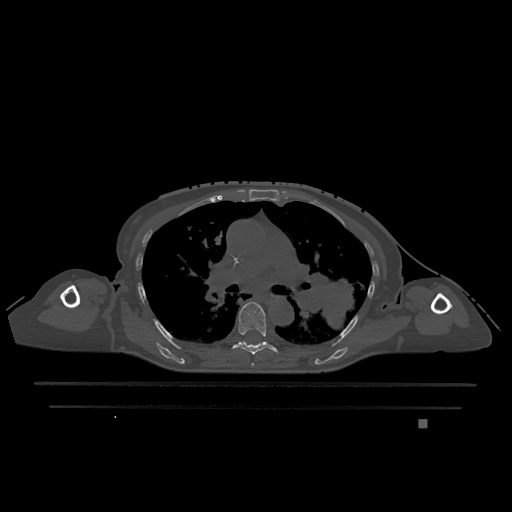
CT including the spine, one axial slice. Slice 788 of 1317 in the series (ordered by position). Bone window (W 1800 / L 400 HU). 512 × 512 image matrix. Patient: female, 74 years. Case-level facts recorded for this patient, not image findings: primary cancer: lung; vertebrae with lytic lesions (as recorded): T1, T4, T5, T6, L4, L5.
Annotated regions visible in this slice (semi-automatic segmentation, software-assisted and operator-edited):
- T5 vertebra: bounding box (x1, y1, x2, y2) in pixels: (251, 363, 254, 367)
- T6 vertebra: (232, 302, 278, 355)